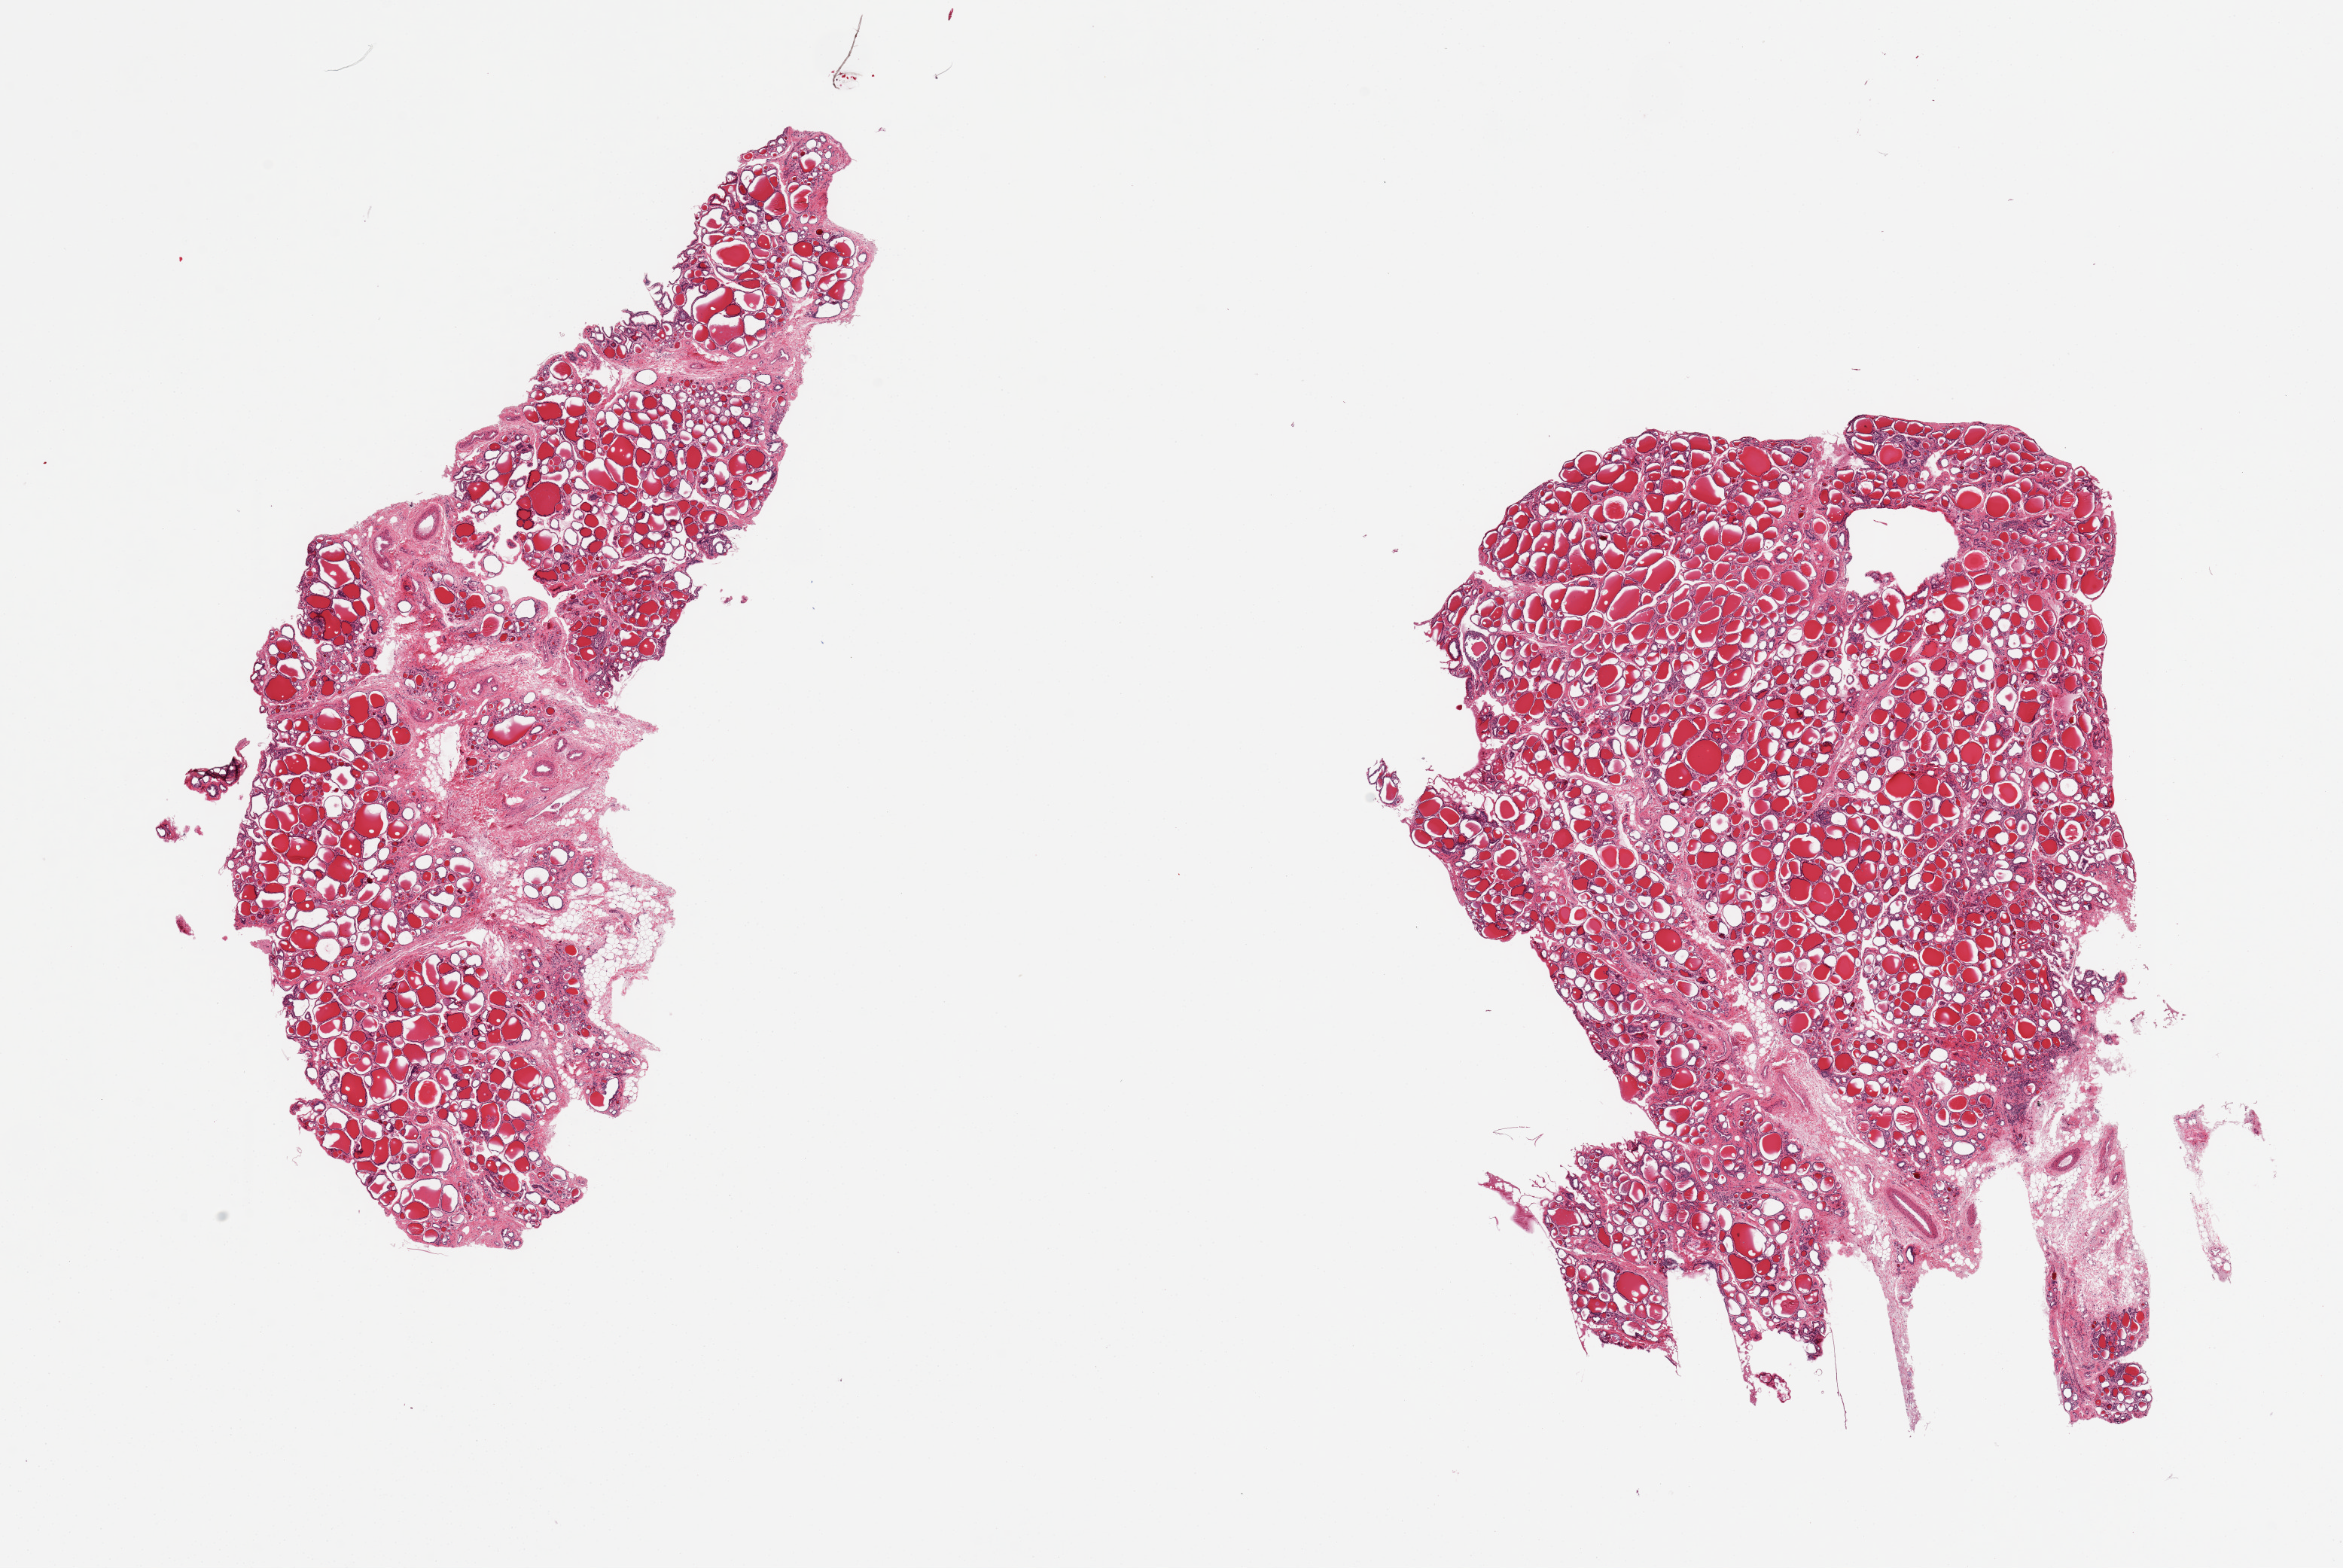
Whole-slide image, haematoxylin and eosin stain, whole scanned area (about 24.6 x 16.5 mm, slide scanned at 20x) shown as a low-resolution overview. PAXgene-fixed paraffin-embedded (PFPE) section. Target tissue: thyroid. Tissue donor sample. Donor sex: female.
Reviewer comment on this tissue sample: 2 pieces, ~10% of smaller piece is fat and vessels.